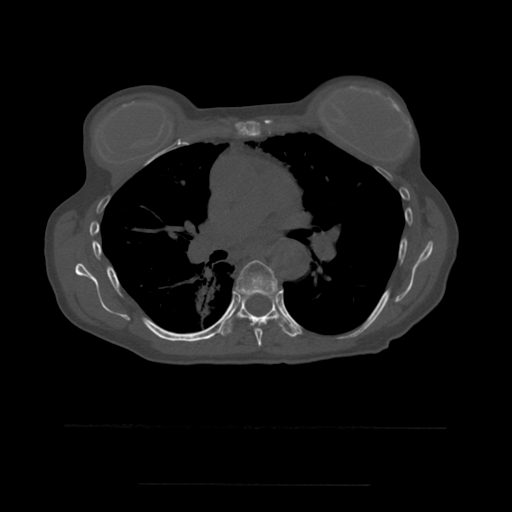
CT including the spine, one axial slice; position 366 of 544 along the scan axis; bone window (W 1800 / L 400 HU); 1.25 mm slice thickness; 512 × 512 image matrix. Patient age 58 years. From the clinical record (not read from this slice): primary cancer: lung.
Outlined on this slice (semi-automatic segmentation, software-assisted and operator-edited):
- T6 vertebra: box from (x=235, y=260) to (x=281, y=347) px
- T7 vertebra: (x=218, y=292)–(x=300, y=338)